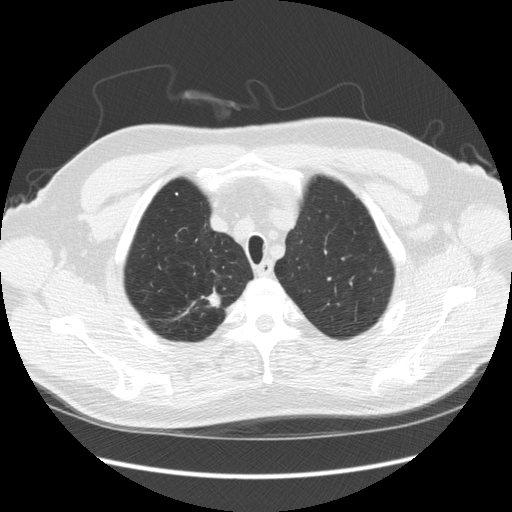
Chest CT (low-dose screening protocol), one axial image; third annual screen; lung window (W 1500 / L -600 HU); 512 × 512 image matrix. Male participant, aged 64 years at enrolment.
- Expert reader's lesion annotation, bounding box (x1, y1, x2, y2) in pixels: (189, 284, 229, 319).
- The screening reader recorded 4 non-calcified nodules or masses ≥4 mm on this exam; which of them this box marks is not recorded.
- Later outcome: lung cancer diagnosed 15 days after this screen — adenocarcinoma, NOS, right upper lobe, moderately differentiated (G2), stage IA (AJCC 6th edition), 14 mm at pathology.